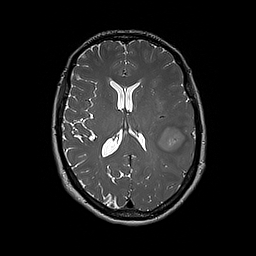
Brain MRI from a brain-tumour surgery series, one axial slice. Slice 92 of 192 in the series (ordered by position). 1 mm slice thickness. 256 × 256 image matrix, field of view 250 × 250 mm. From the clinical record (not read from this slice): histopathology: Glioblastoma; WHO grade: 4; IDH mutation: no.
Structures marked on this image (outlined manually by an expert reader):
- tumour: box from (x=161, y=117) to (x=195, y=170) px